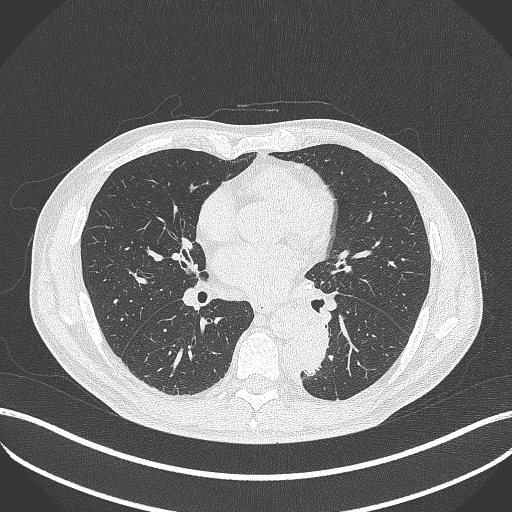
Chest CT, one axial slice. Slice 200 of 451 in the series (ordered by position). Reconstruction kernel B70f. Lung window (W 1500 / L -600 HU). 1 mm slice thickness. 512 × 512 image matrix, field of view 400 × 400 mm. Patient: male, 72 years. From the clinical record (not read from this slice): clinical TNM (as recorded): T2b N0 M1.
Annotated regions visible in this slice (bounding box drawn by a radiologist):
- lung tumour (recorded histology: adenocarcinoma): bounding box (x1, y1, x2, y2) in pixels: (294, 318, 332, 380)